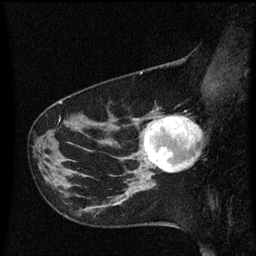
Breast MRI (dynamic contrast-enhanced), one sagittal slice. Position 20 of 60 along the scan axis. Dynamic contrast-enhanced series, image 2 of 3 at this slice position (ordered by acquisition). 1.5 T. TE 4.2 ms, TR 8.4 ms. 2 mm slice thickness. 256 × 256 image matrix. Patient: female, 41 years. Case-level facts recorded for this patient, not image findings: setting: breast cancer imaged before/during neoadjuvant chemotherapy; receptor status: triple-negative.
Outlined on this slice (semi-automatically segmented with operator editing):
- analysis volume of interest (the breast-tissue region the enhancement analysis was run in; not a lesion): box from (x=138, y=112) to (x=200, y=177) px
- tumour enhancement mask (voxels above the 70 % enhancement threshold inside the analysis volume of interest): (x=144, y=116)–(x=200, y=173)